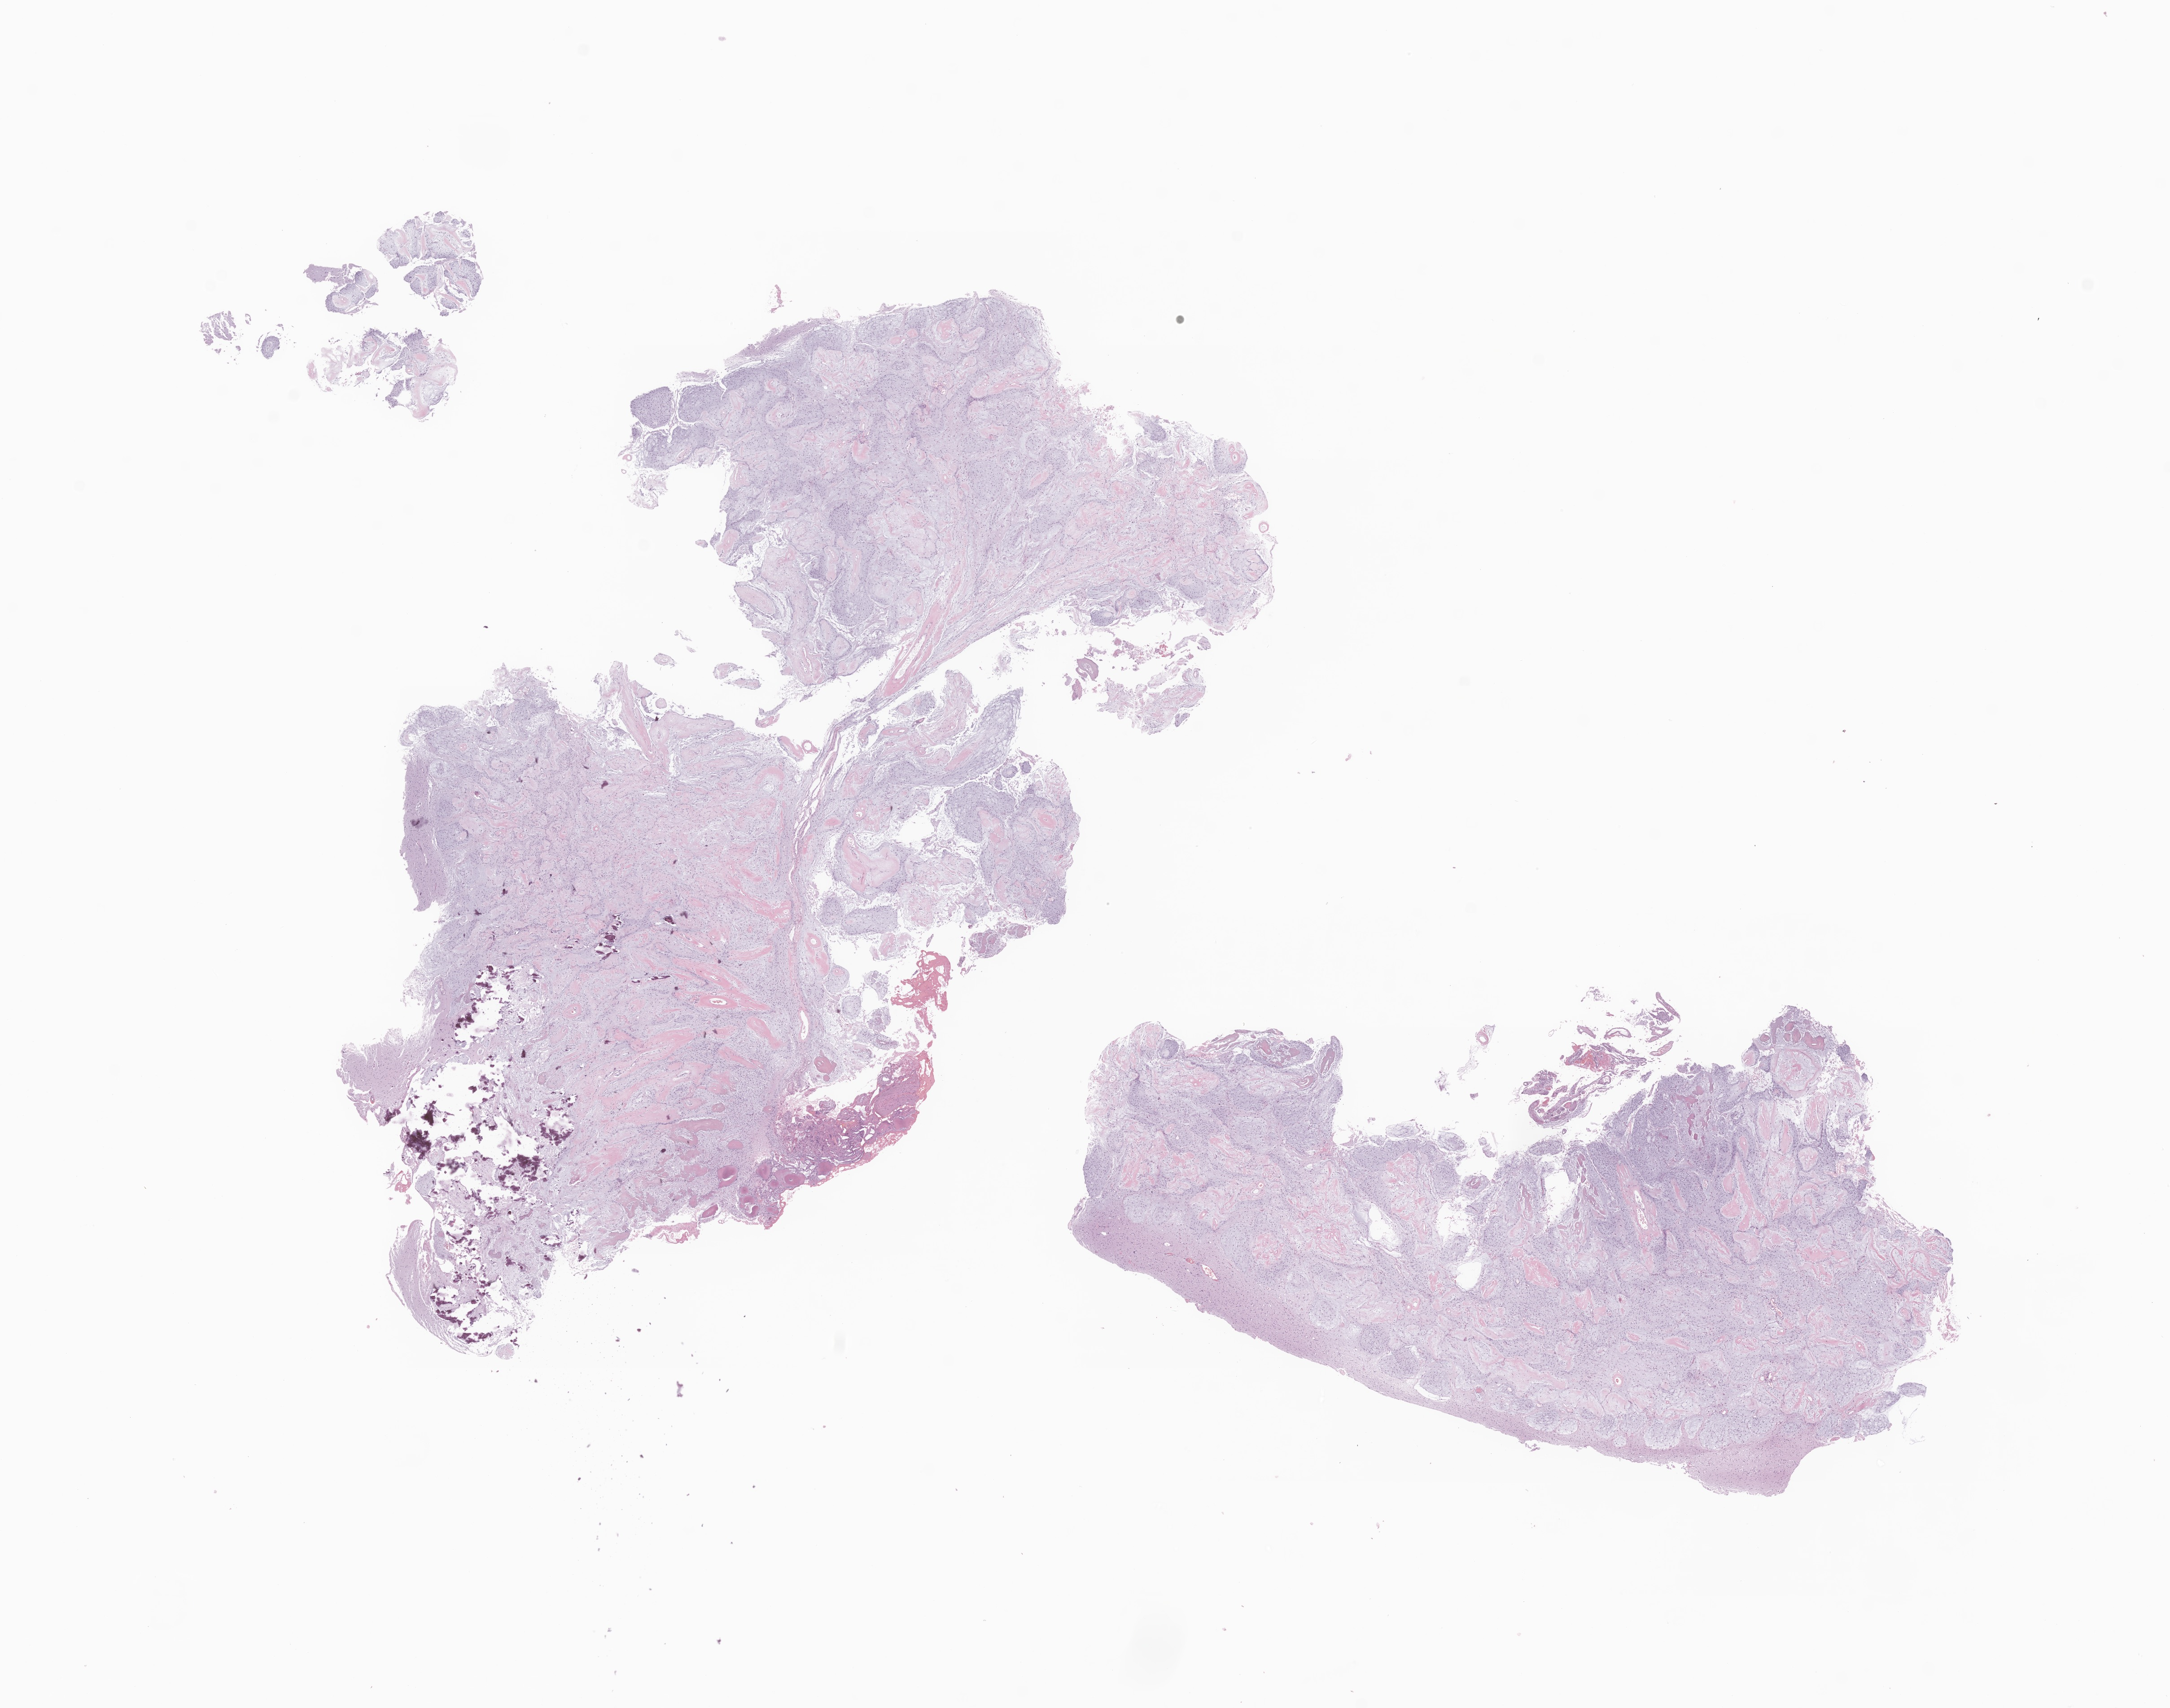
Haematoxylin and eosin whole-slide image of tumor tissue from the brain, whole scanned area (about 20.4 x 16.0 mm) shown as a low-resolution overview; formalin-fixed, paraffin-embedded (FFPE) tissue. Patient male; age 51 months (4 years 3 months).
- recorded diagnosis: Neoplasm, uncertain whether benign or malignant